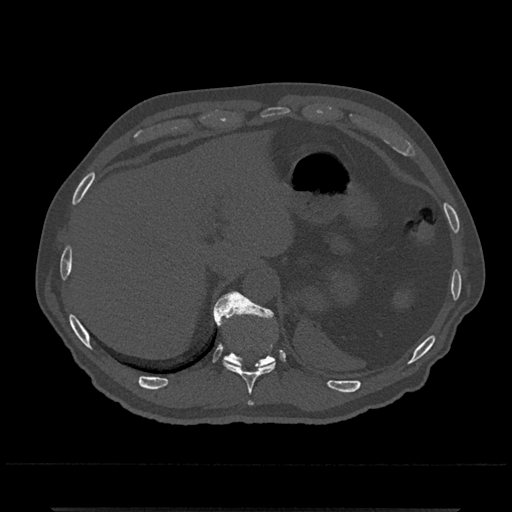
CT including the spine, one axial slice; slice 530 of 797 in the series (ordered by position); 120 kVp; bone window (W 1800 / L 400 HU); 512 × 512 image matrix, field of view 393 × 393 mm. Male patient, age 67 years. Case-level facts recorded for this patient, not image findings: primary cancer: prostate.
Outlined on this slice (semi-automatically segmented with operator editing):
- T10 vertebra: bounding box [x1, y1, x2, y2] px = [217, 292, 276, 406]
- T11 vertebra: [213, 293, 276, 368]